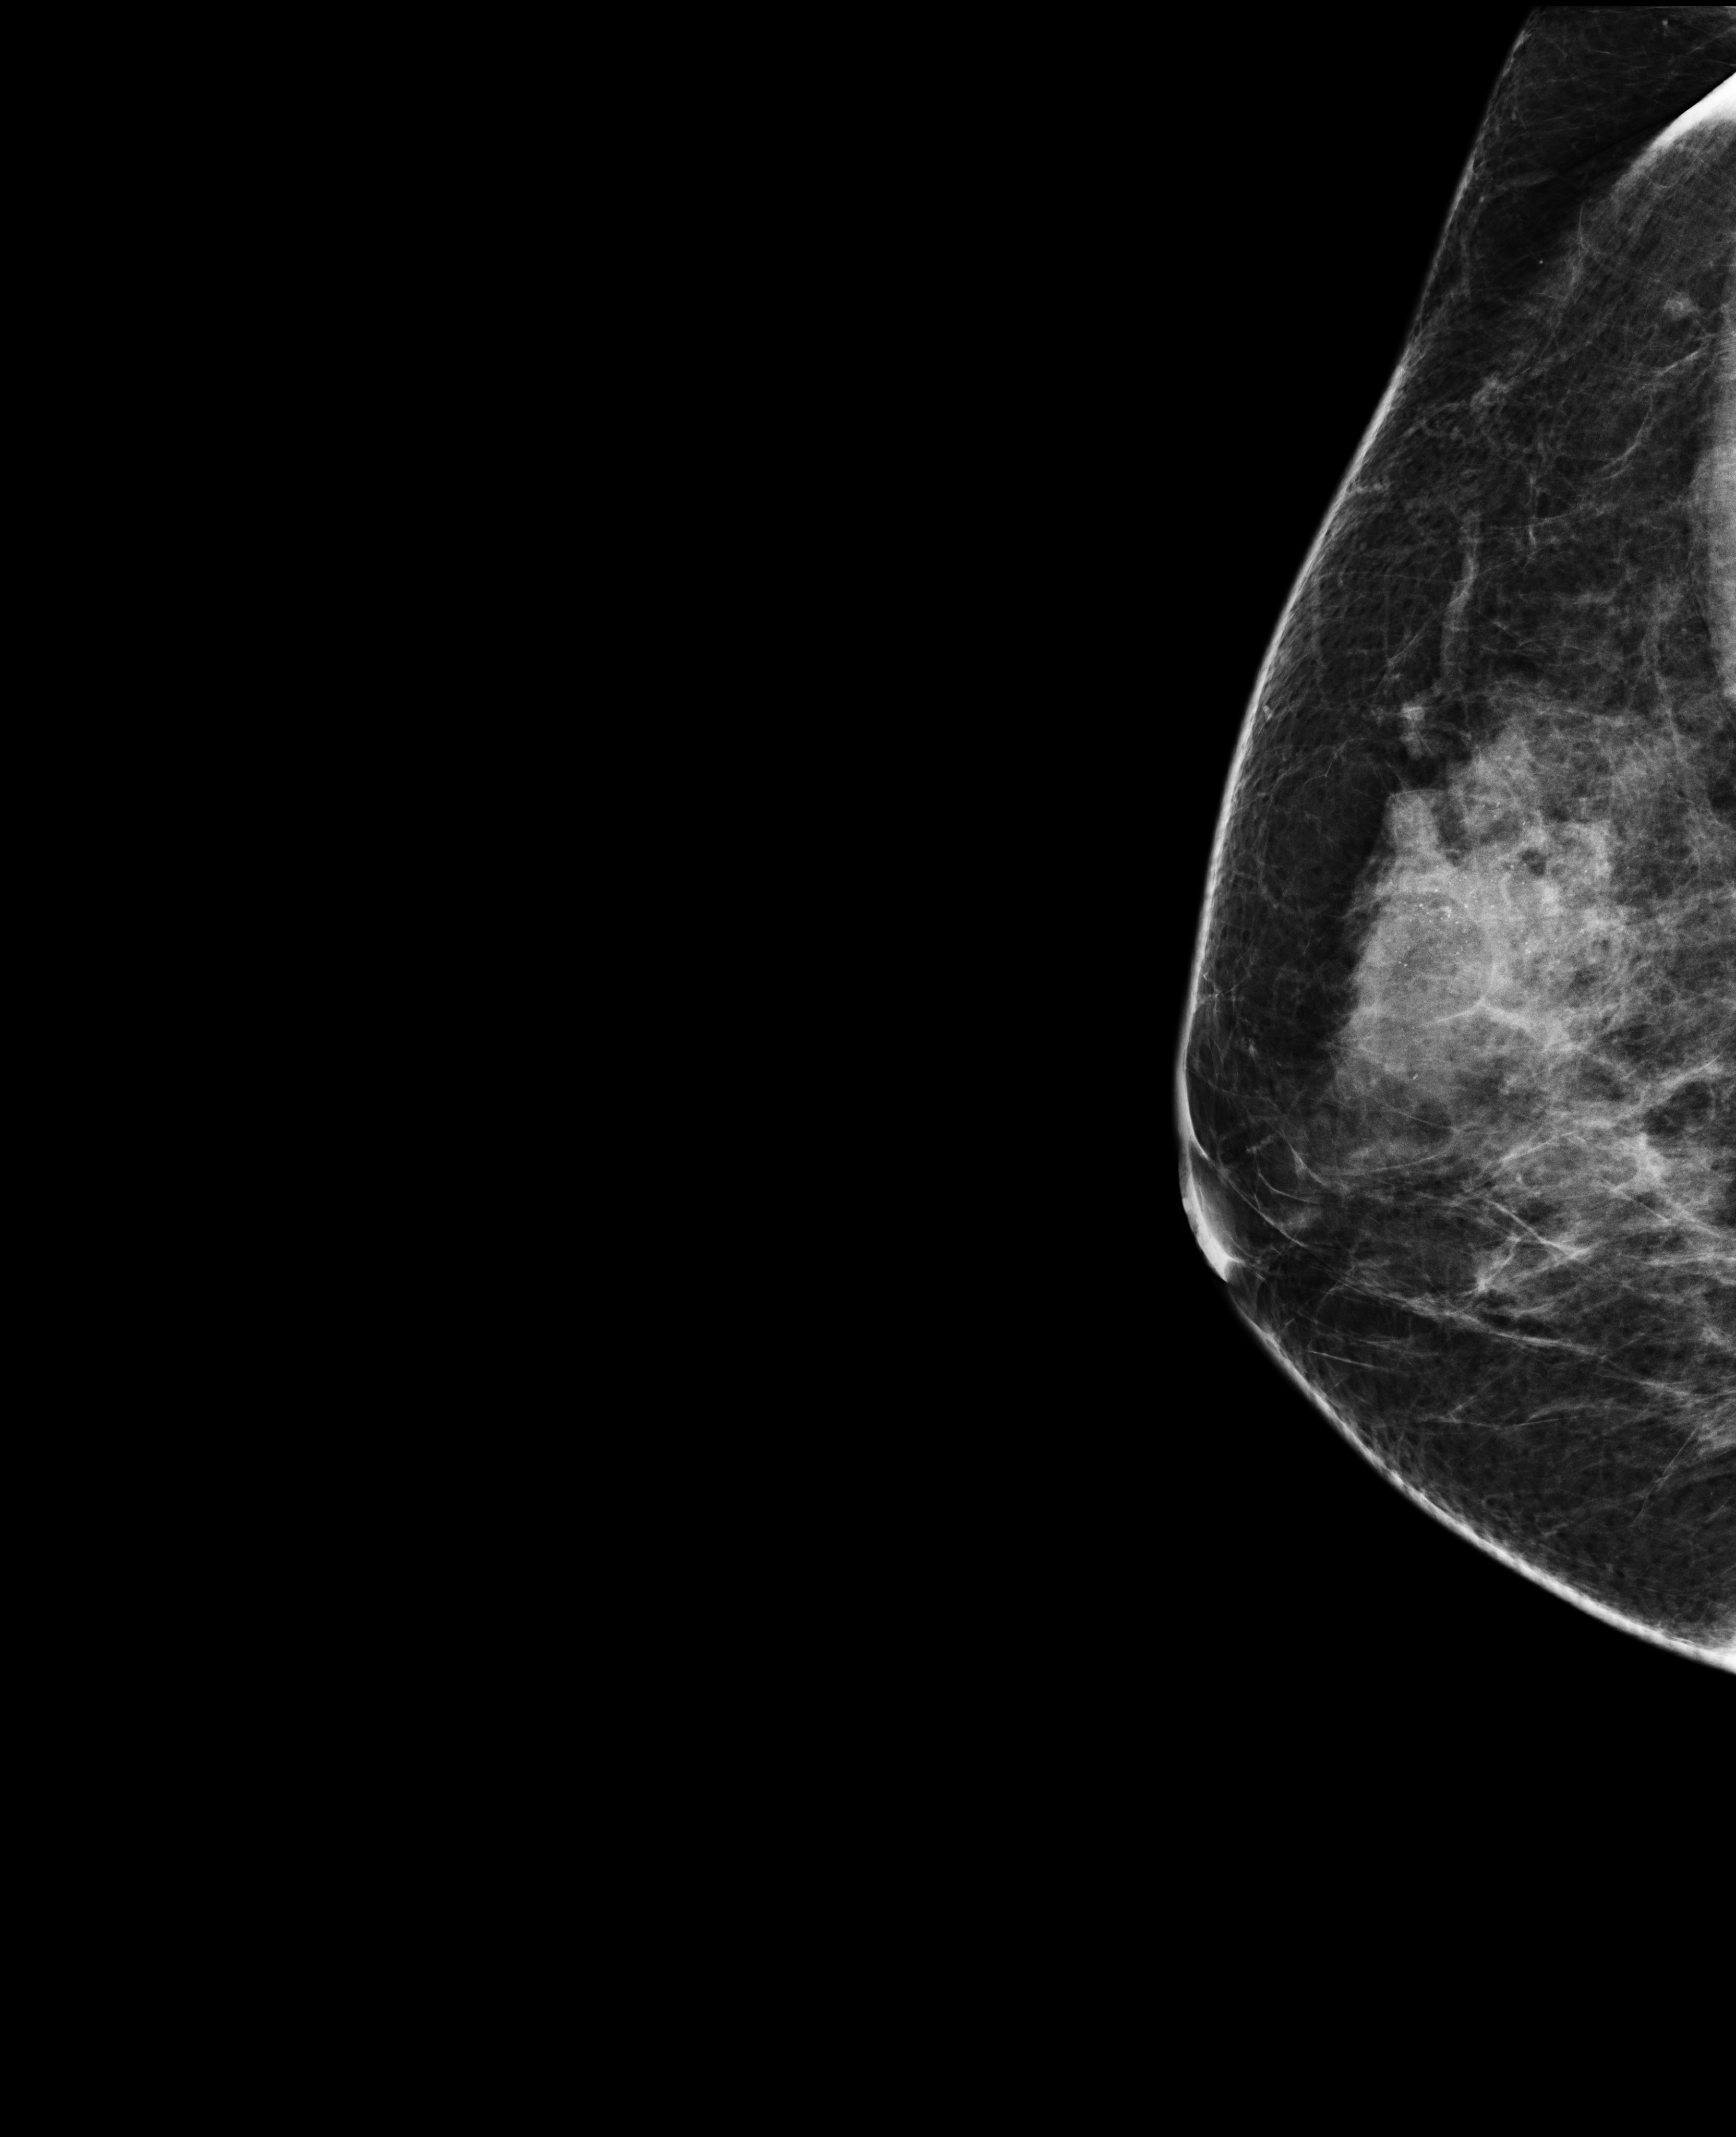
Digital mammogram (FFDM); right breast; laterally exaggerated craniocaudal (XCCL) view; screening examination; compressed breast thickness 61 mm; system: Selenia Dimensions. Patient: female, 48 years.
- BI-RADS breast density category at the screening exam (both breasts, scale 1–4): 3
- final BI-RADS assessment for this screening round (tomosynthesis exam, both breasts): category 4
- recall: recalled for additional imaging after this screen